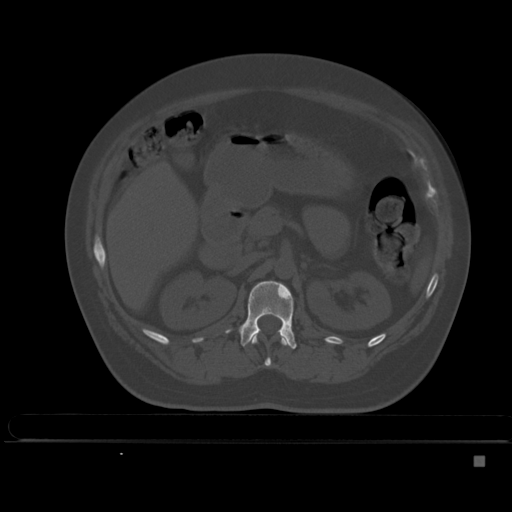
CT including the spine, one axial slice. Position 200 of 495 along the scan axis. Bone window (W 1800 / L 400 HU). 512 × 512 image matrix, field of view 404 × 404 mm. Female patient, age 33 years. From the clinical record (not read from this slice): primary cancer: breast; vertebrae with lytic lesions (as recorded): T1.
Structures marked on this image (semi-automatically segmented with operator editing):
- L1 vertebra: box from (x=225, y=280) to (x=297, y=349) px
- T12 vertebra: (x=250, y=335)–(x=290, y=367)